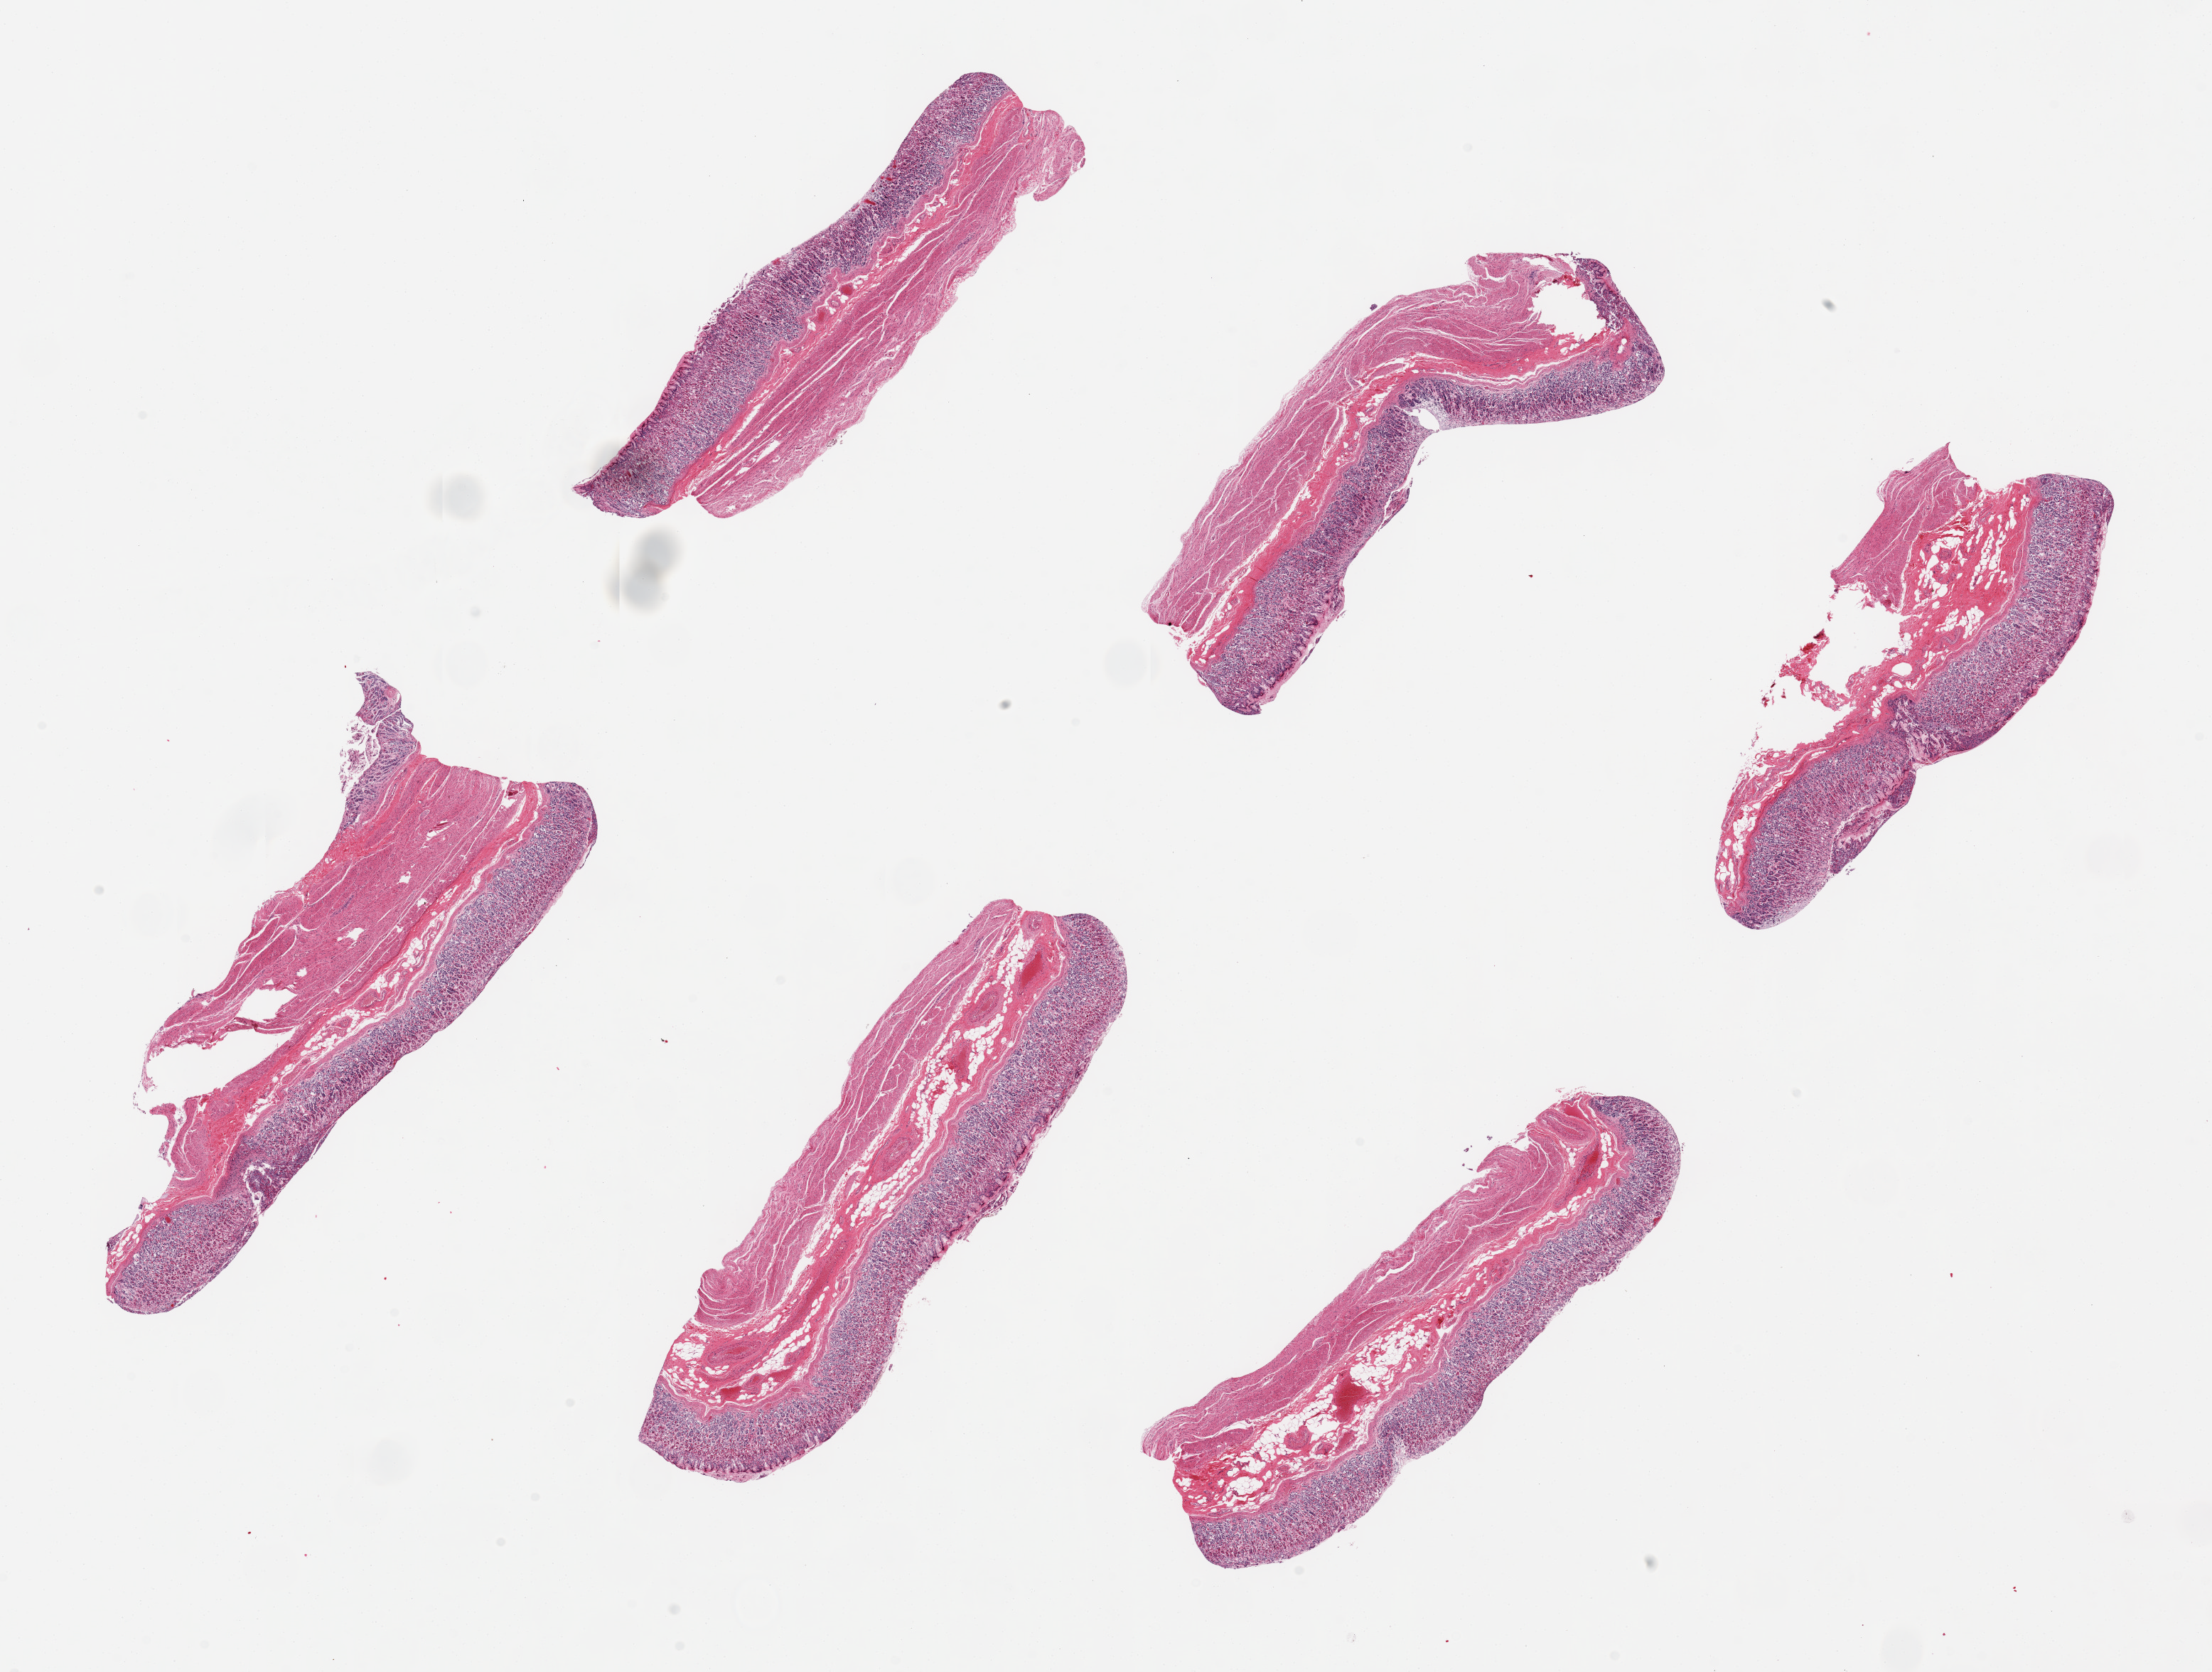
H&E whole-slide image, brightfield, low-resolution overview of the scanned area, about 24.6 x 18.6 mm; PAXgene-fixed paraffin-embedded (PFPE) section; section of stomach (target tissue); donor tissue sample. Donor: female.
Review note (as recorded): 6 pieces up to 7x2 mm; mucosa moderately autolyzed.